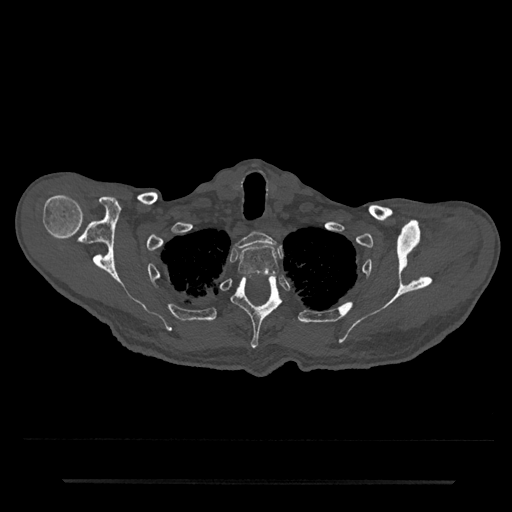
CT including the spine, one axial slice. Slice 669 of 797 in the series (ordered by position). Reconstruction kernel Br40s/3. Bone window (W 1800 / L 400 HU). 0.5 mm slice thickness. 512 × 512 image matrix, field of view 427 × 427 mm. Patient: male, 74 years. From the clinical record (not read from this slice): primary cancer: prostate.
Outlined on this slice (semi-automatic segmentation, software-assisted and operator-edited):
- T1 vertebra: box from (x=236, y=231) to (x=276, y=249) px
- T2 vertebra: (x=238, y=245)–(x=280, y=275)
- T3 vertebra: (x=231, y=275)–(x=282, y=349)
- T4 vertebra: (x=291, y=318)–(x=295, y=323)